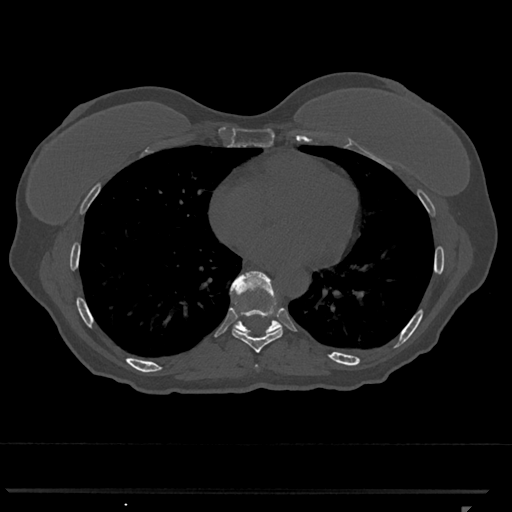
CT including the spine, one axial slice. Slice 651 of 793 in the series (ordered by position). Reconstruction kernel Br40s/3. 120 kVp. Bone window (W 1800 / L 400 HU). 0.5 mm slice thickness. 512 × 512 image matrix, field of view 380 × 380 mm. Female patient, age 62 years. From the clinical record (not read from this slice): primary cancer: renal.
Structures marked on this image (semi-automatic segmentation, software-assisted and operator-edited):
- T8 vertebra: bounding box [x1, y1, x2, y2] px = [232, 309, 283, 353]
- T9 vertebra: [230, 271, 282, 335]